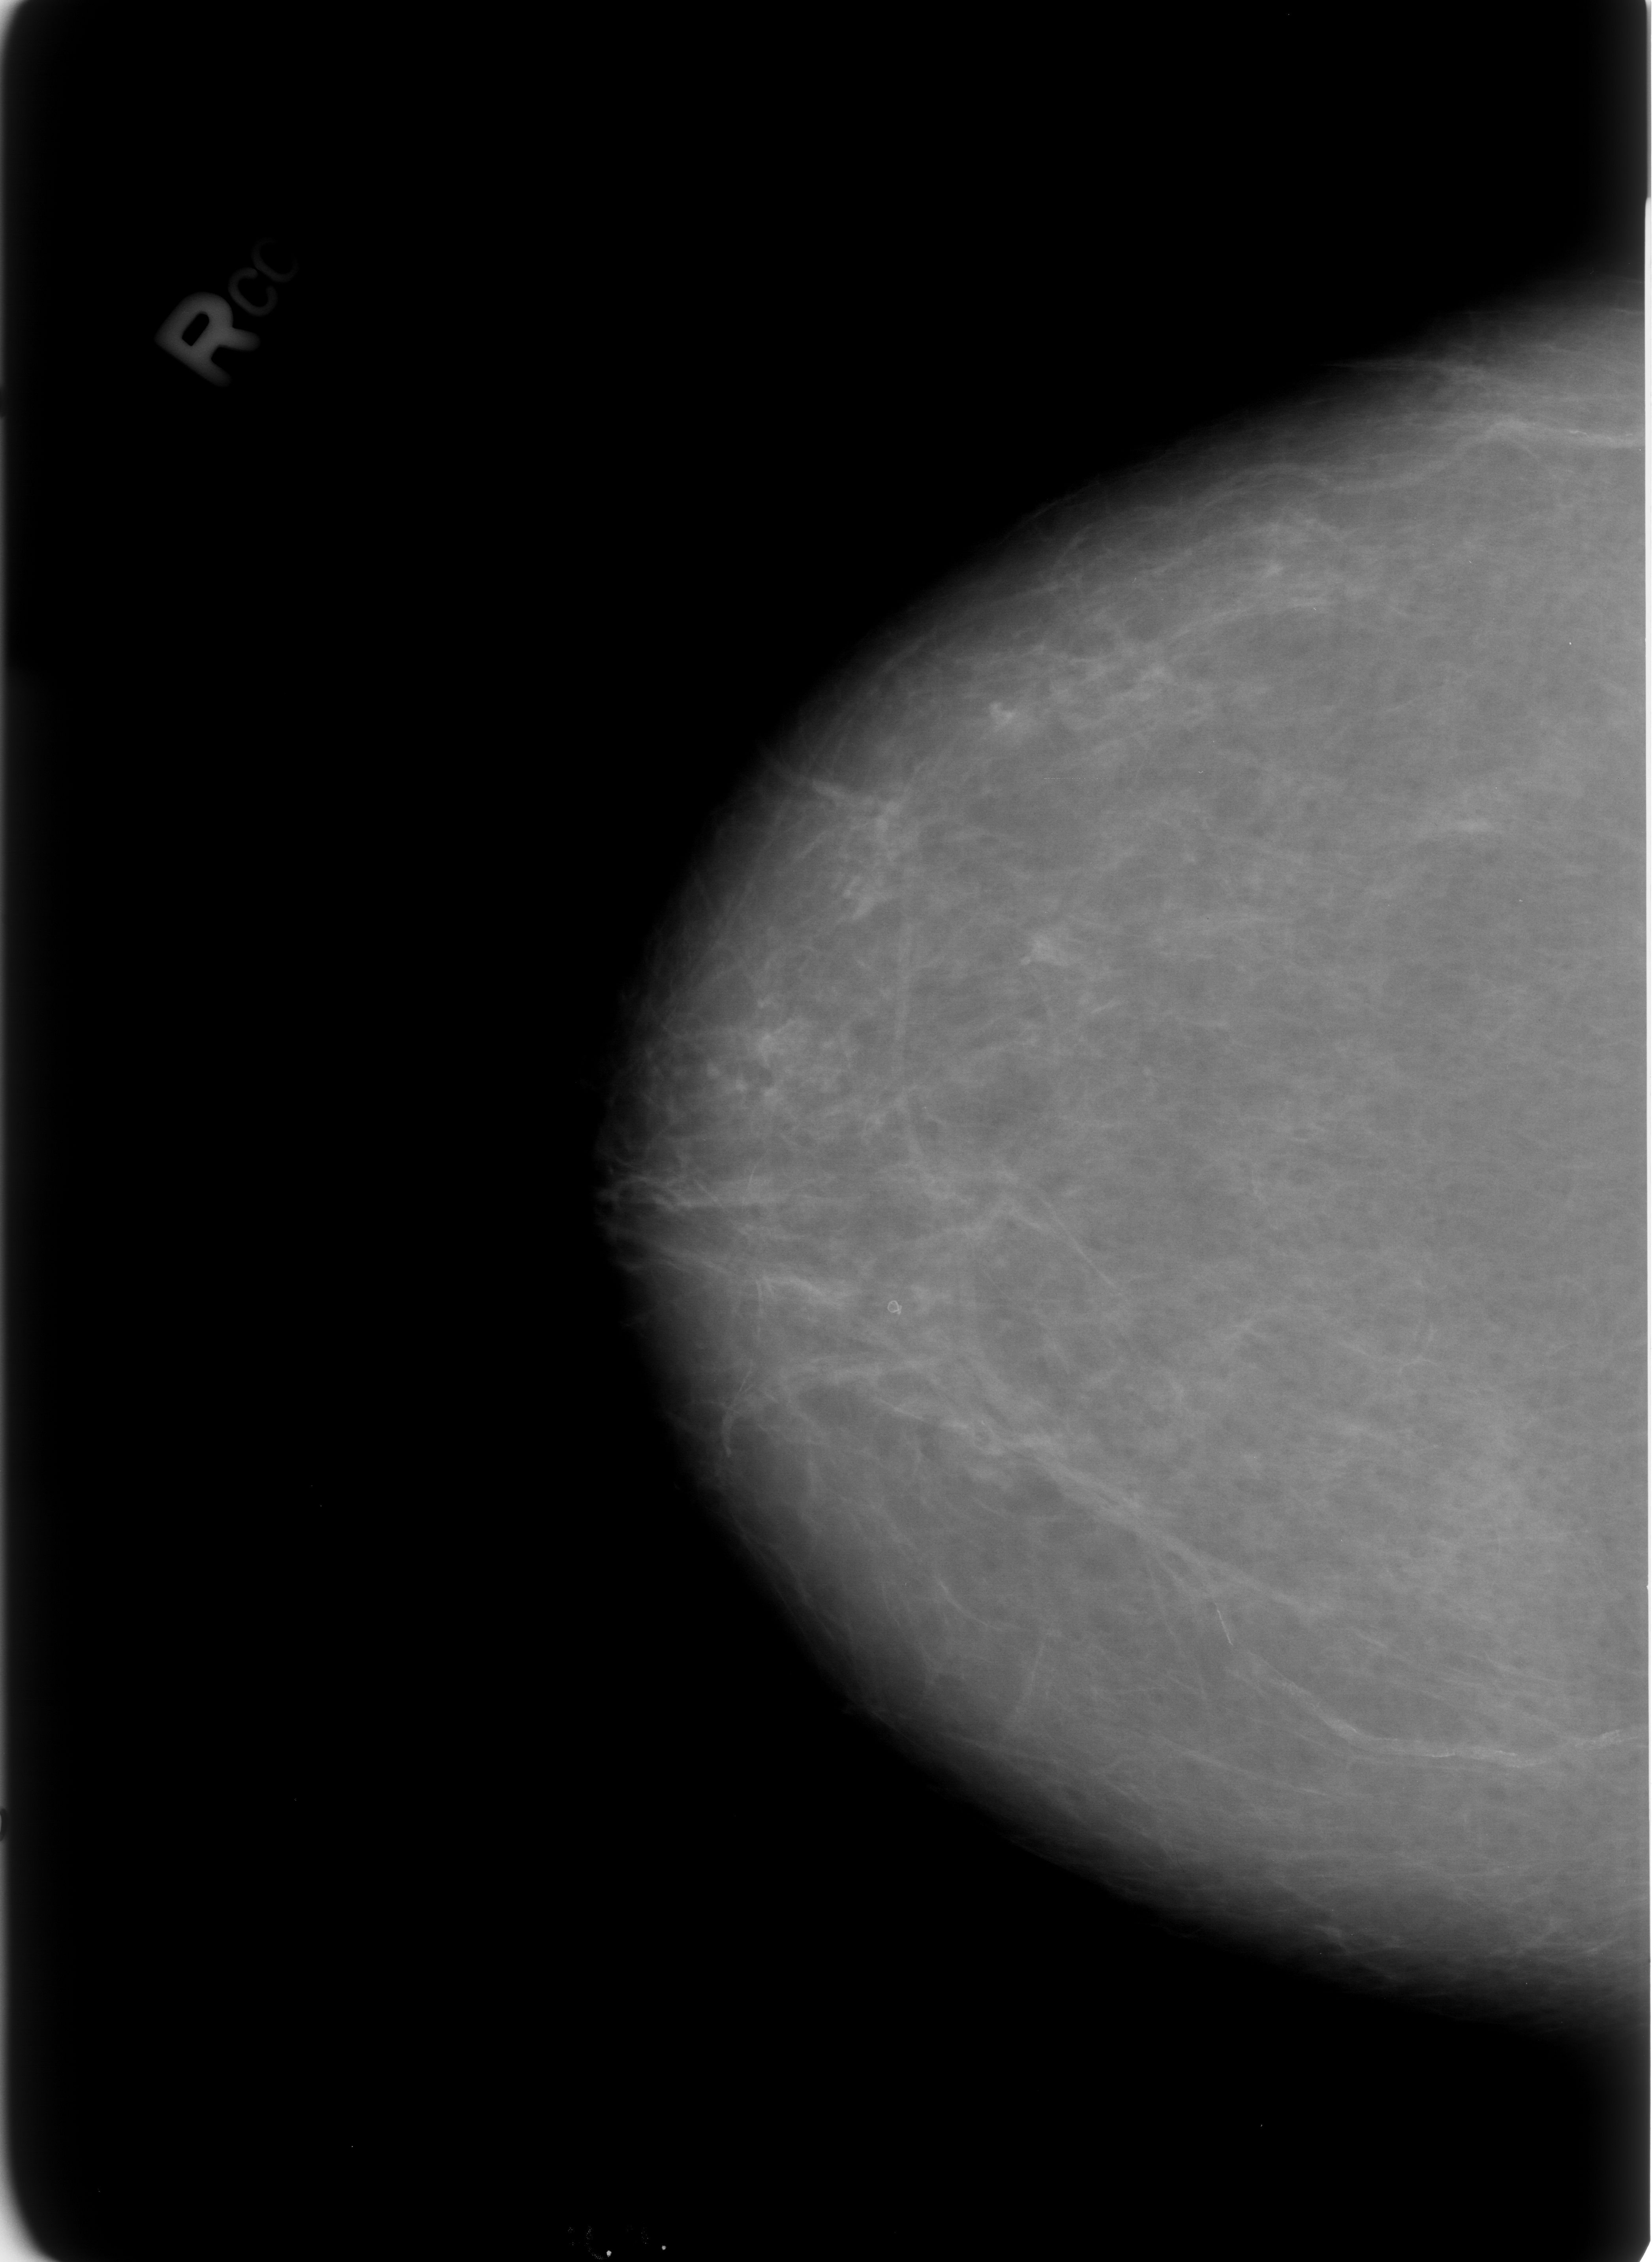
Digitized screen-film mammogram. Right breast. CC view. 1652 × 2262 image matrix.
Expert-marked regions of interest on this film, with their recorded descriptors:
- calcifications, morphology lucent centered; BI-RADS assessment category 2; outcome (as recorded, no biopsy): benign without callback (not worked up further): box from (x=881, y=1292) to (x=911, y=1331) px